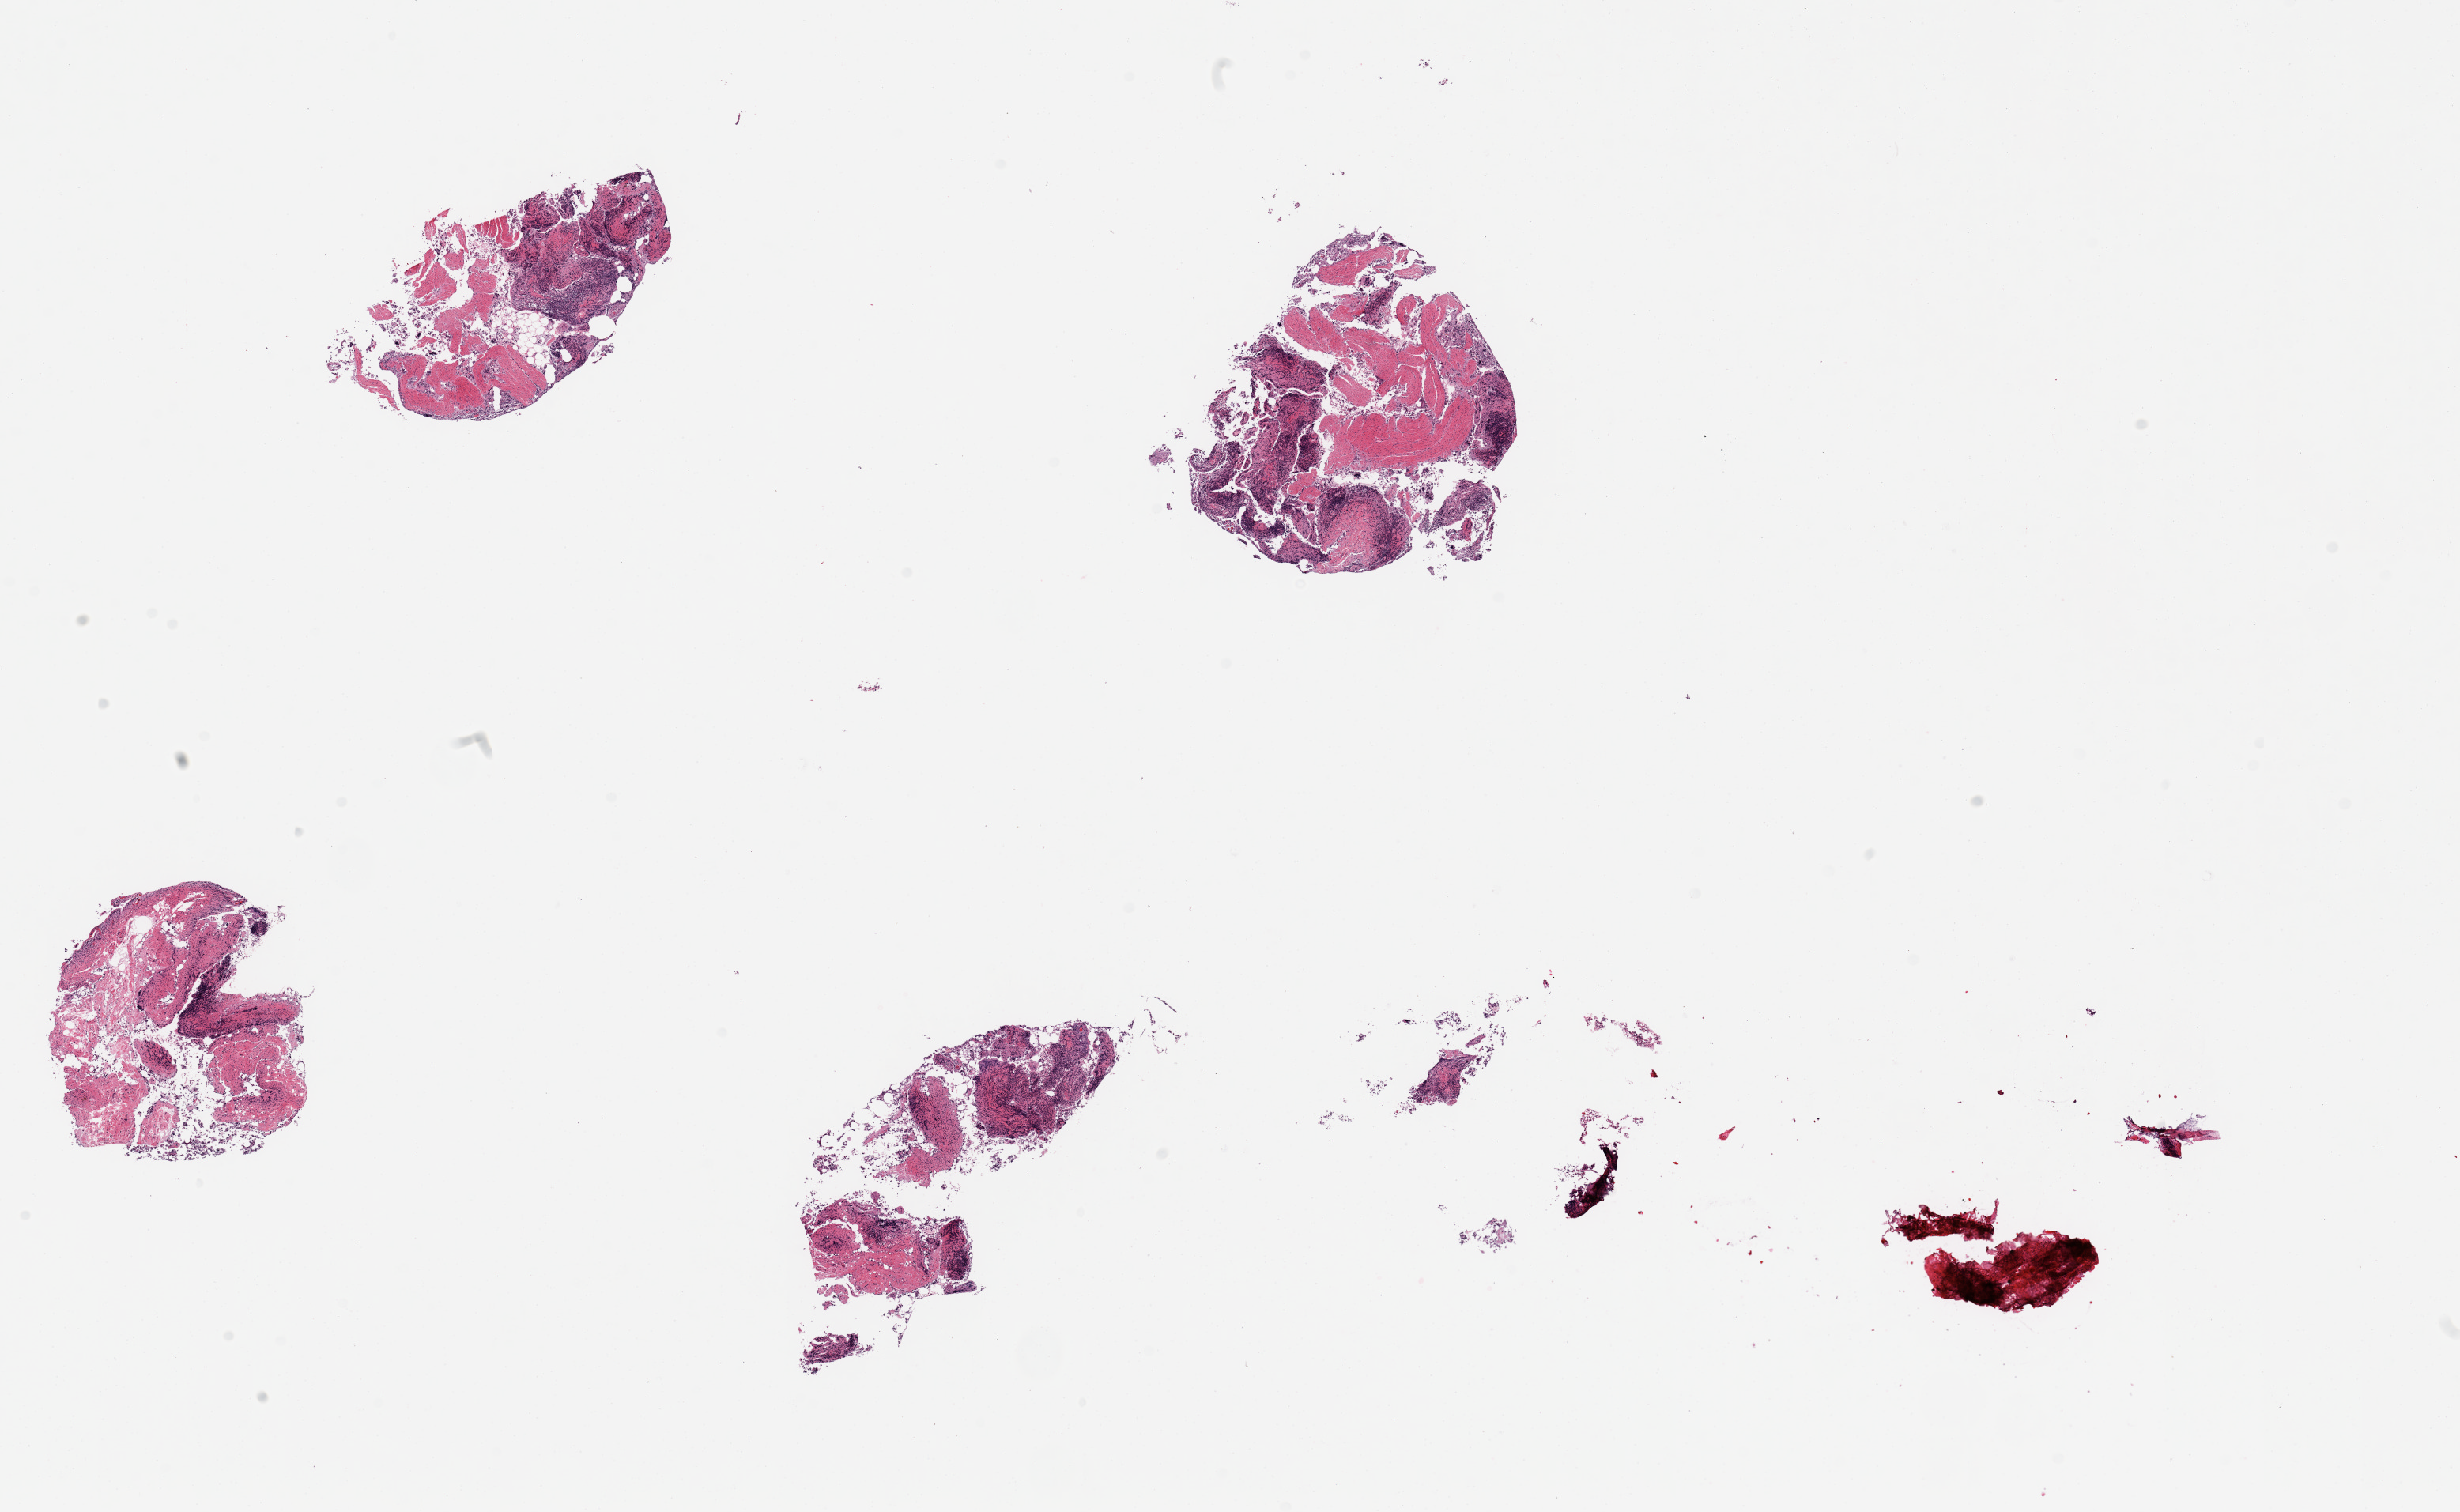
Digitized haematoxylin and eosin-stained section, shown as a low-resolution overview of the whole scanned area (about 24.6 x 15.1 mm). PAXgene-fixed, paraffin-embedded tissue. Section of ileum (target tissue). Tissue donor sample. Male donor.
Pathologist's review note for this sample: 5 pieces; fragments of muscularis and autolyzed mucosa, scattered residual lymphoid tissue present.